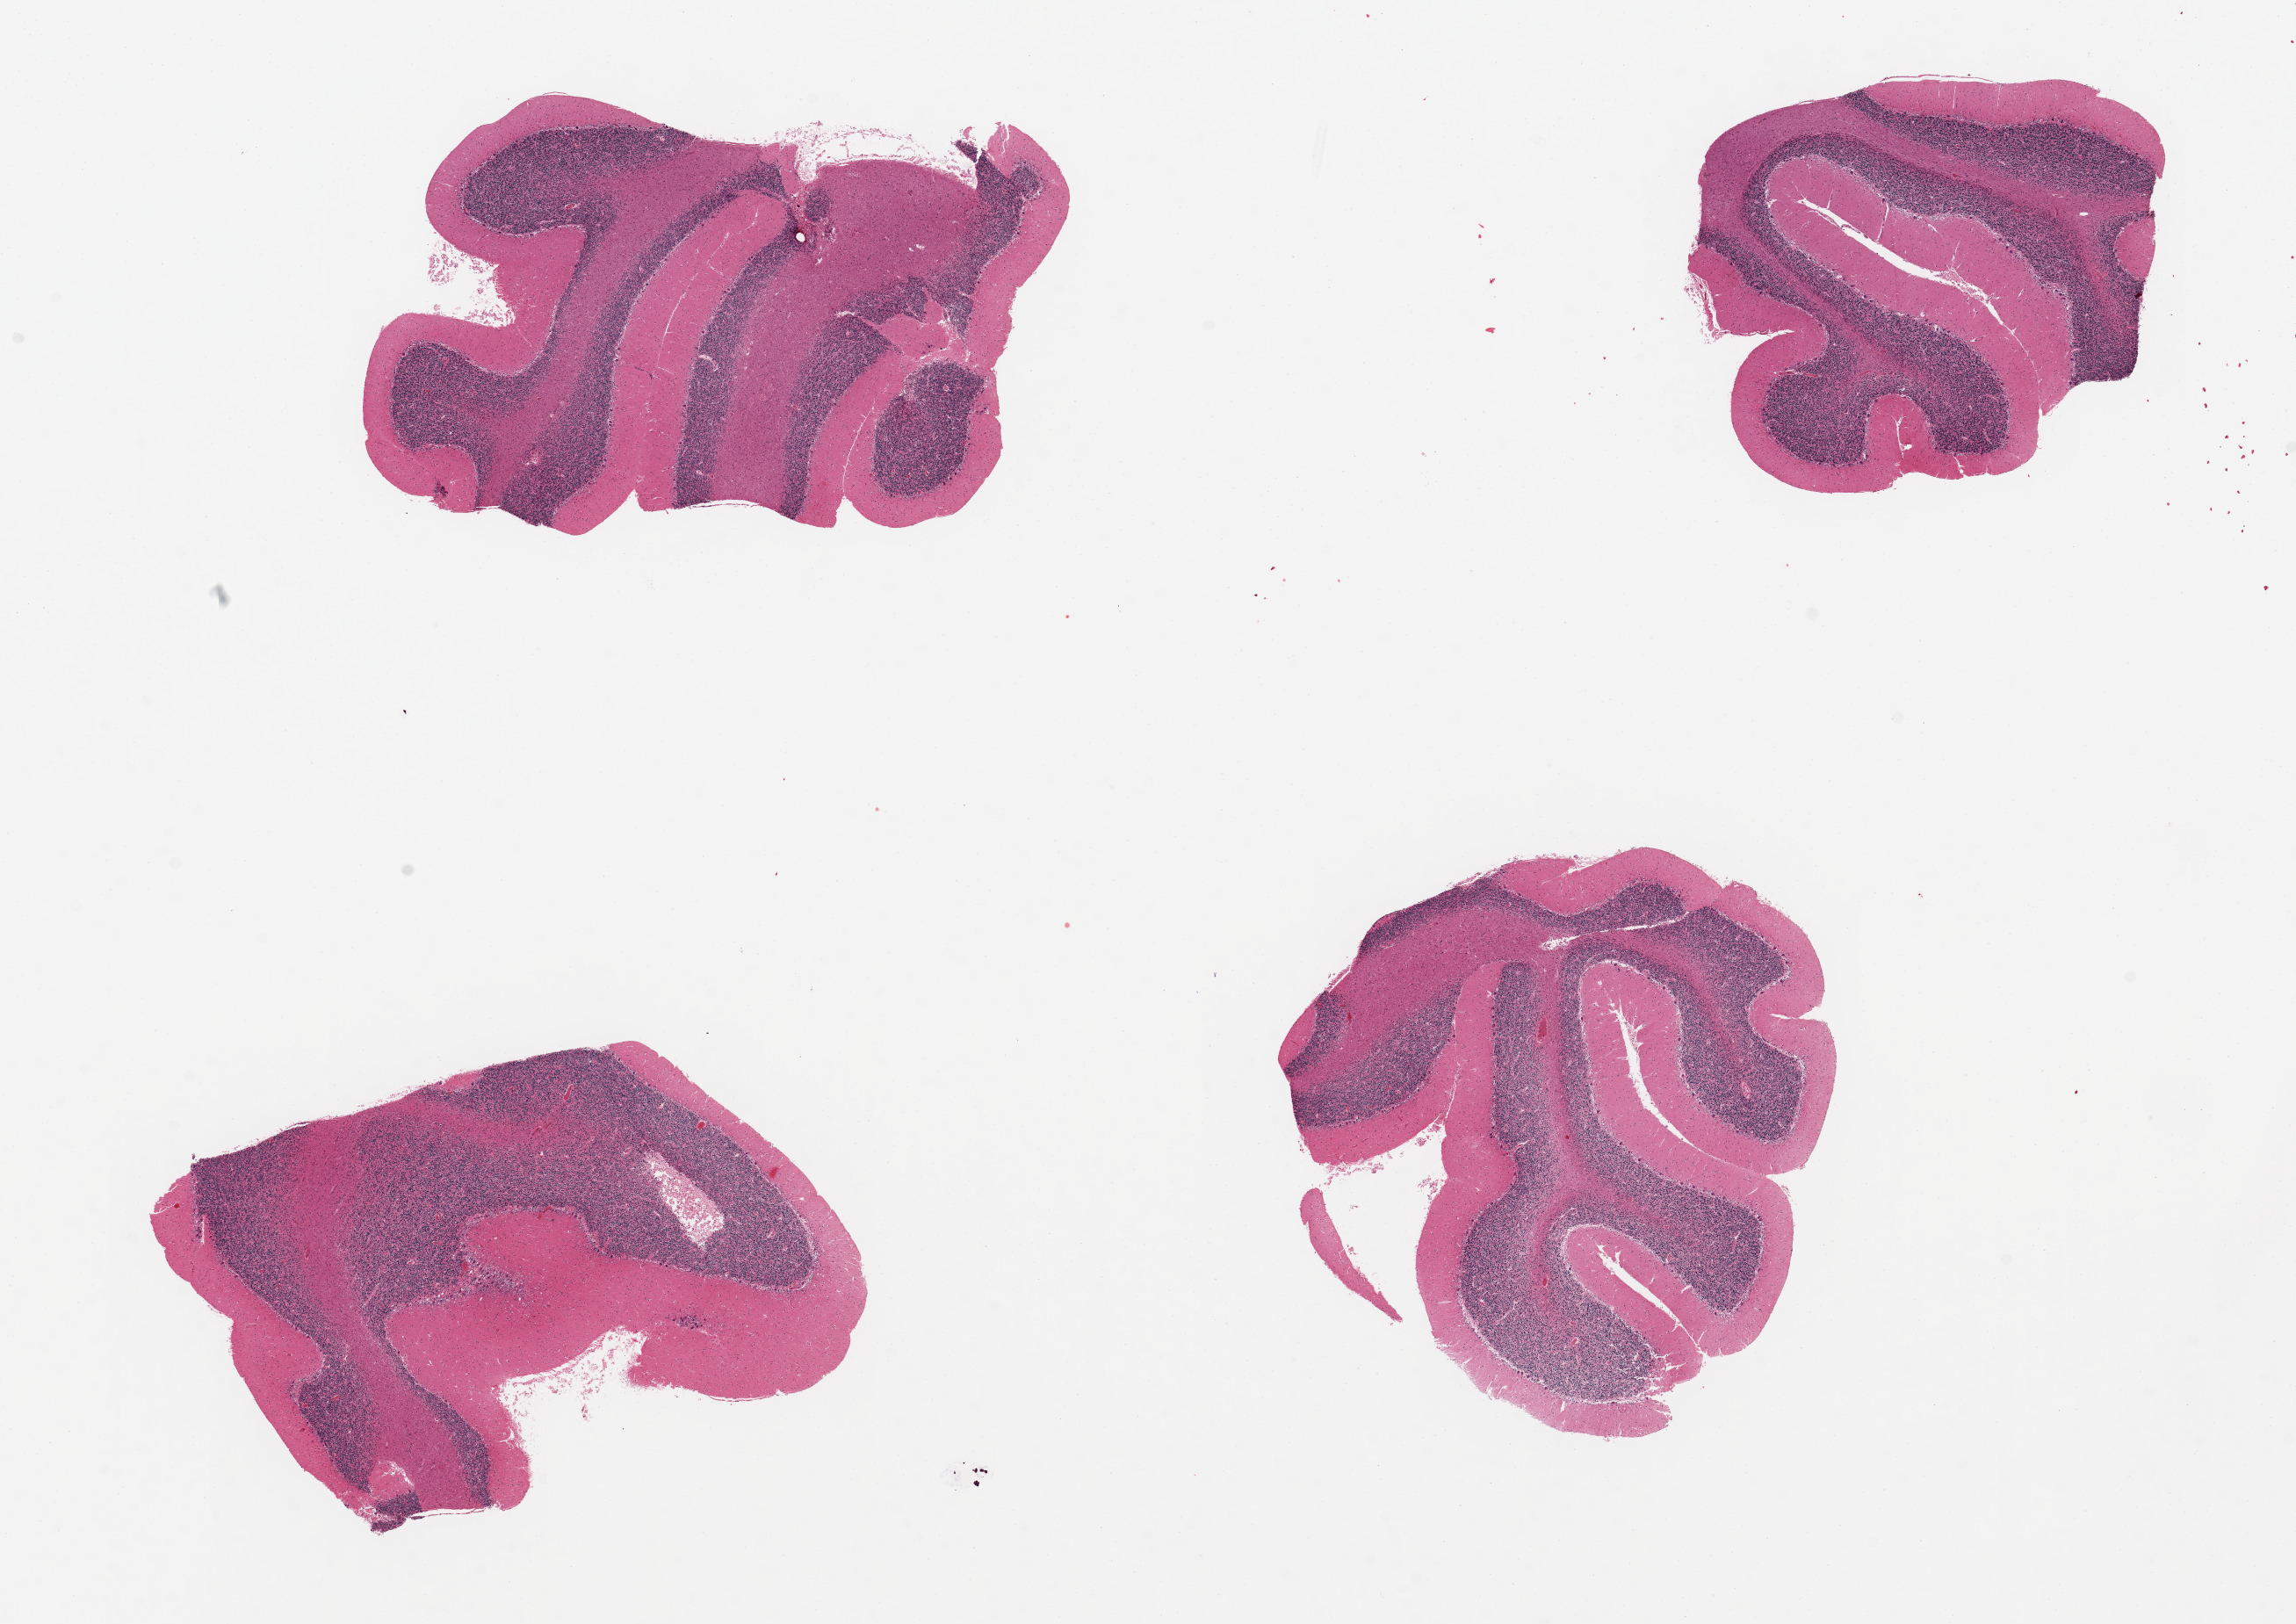
Digitized hematoxylin and eosin (H&E)-stained section, brightfield, shown as a low-resolution overview of the whole scanned area (about 20.7 x 14.6 mm, acquisition: 20x scan). PAXgene-fixed paraffin-embedded (PFPE) section. Target tissue: cerebellum. Donor tissue sample. Donor: male.
* pathologist's review note for this sample: 4 pieces up to 5x4 mm; good Purkinje cells